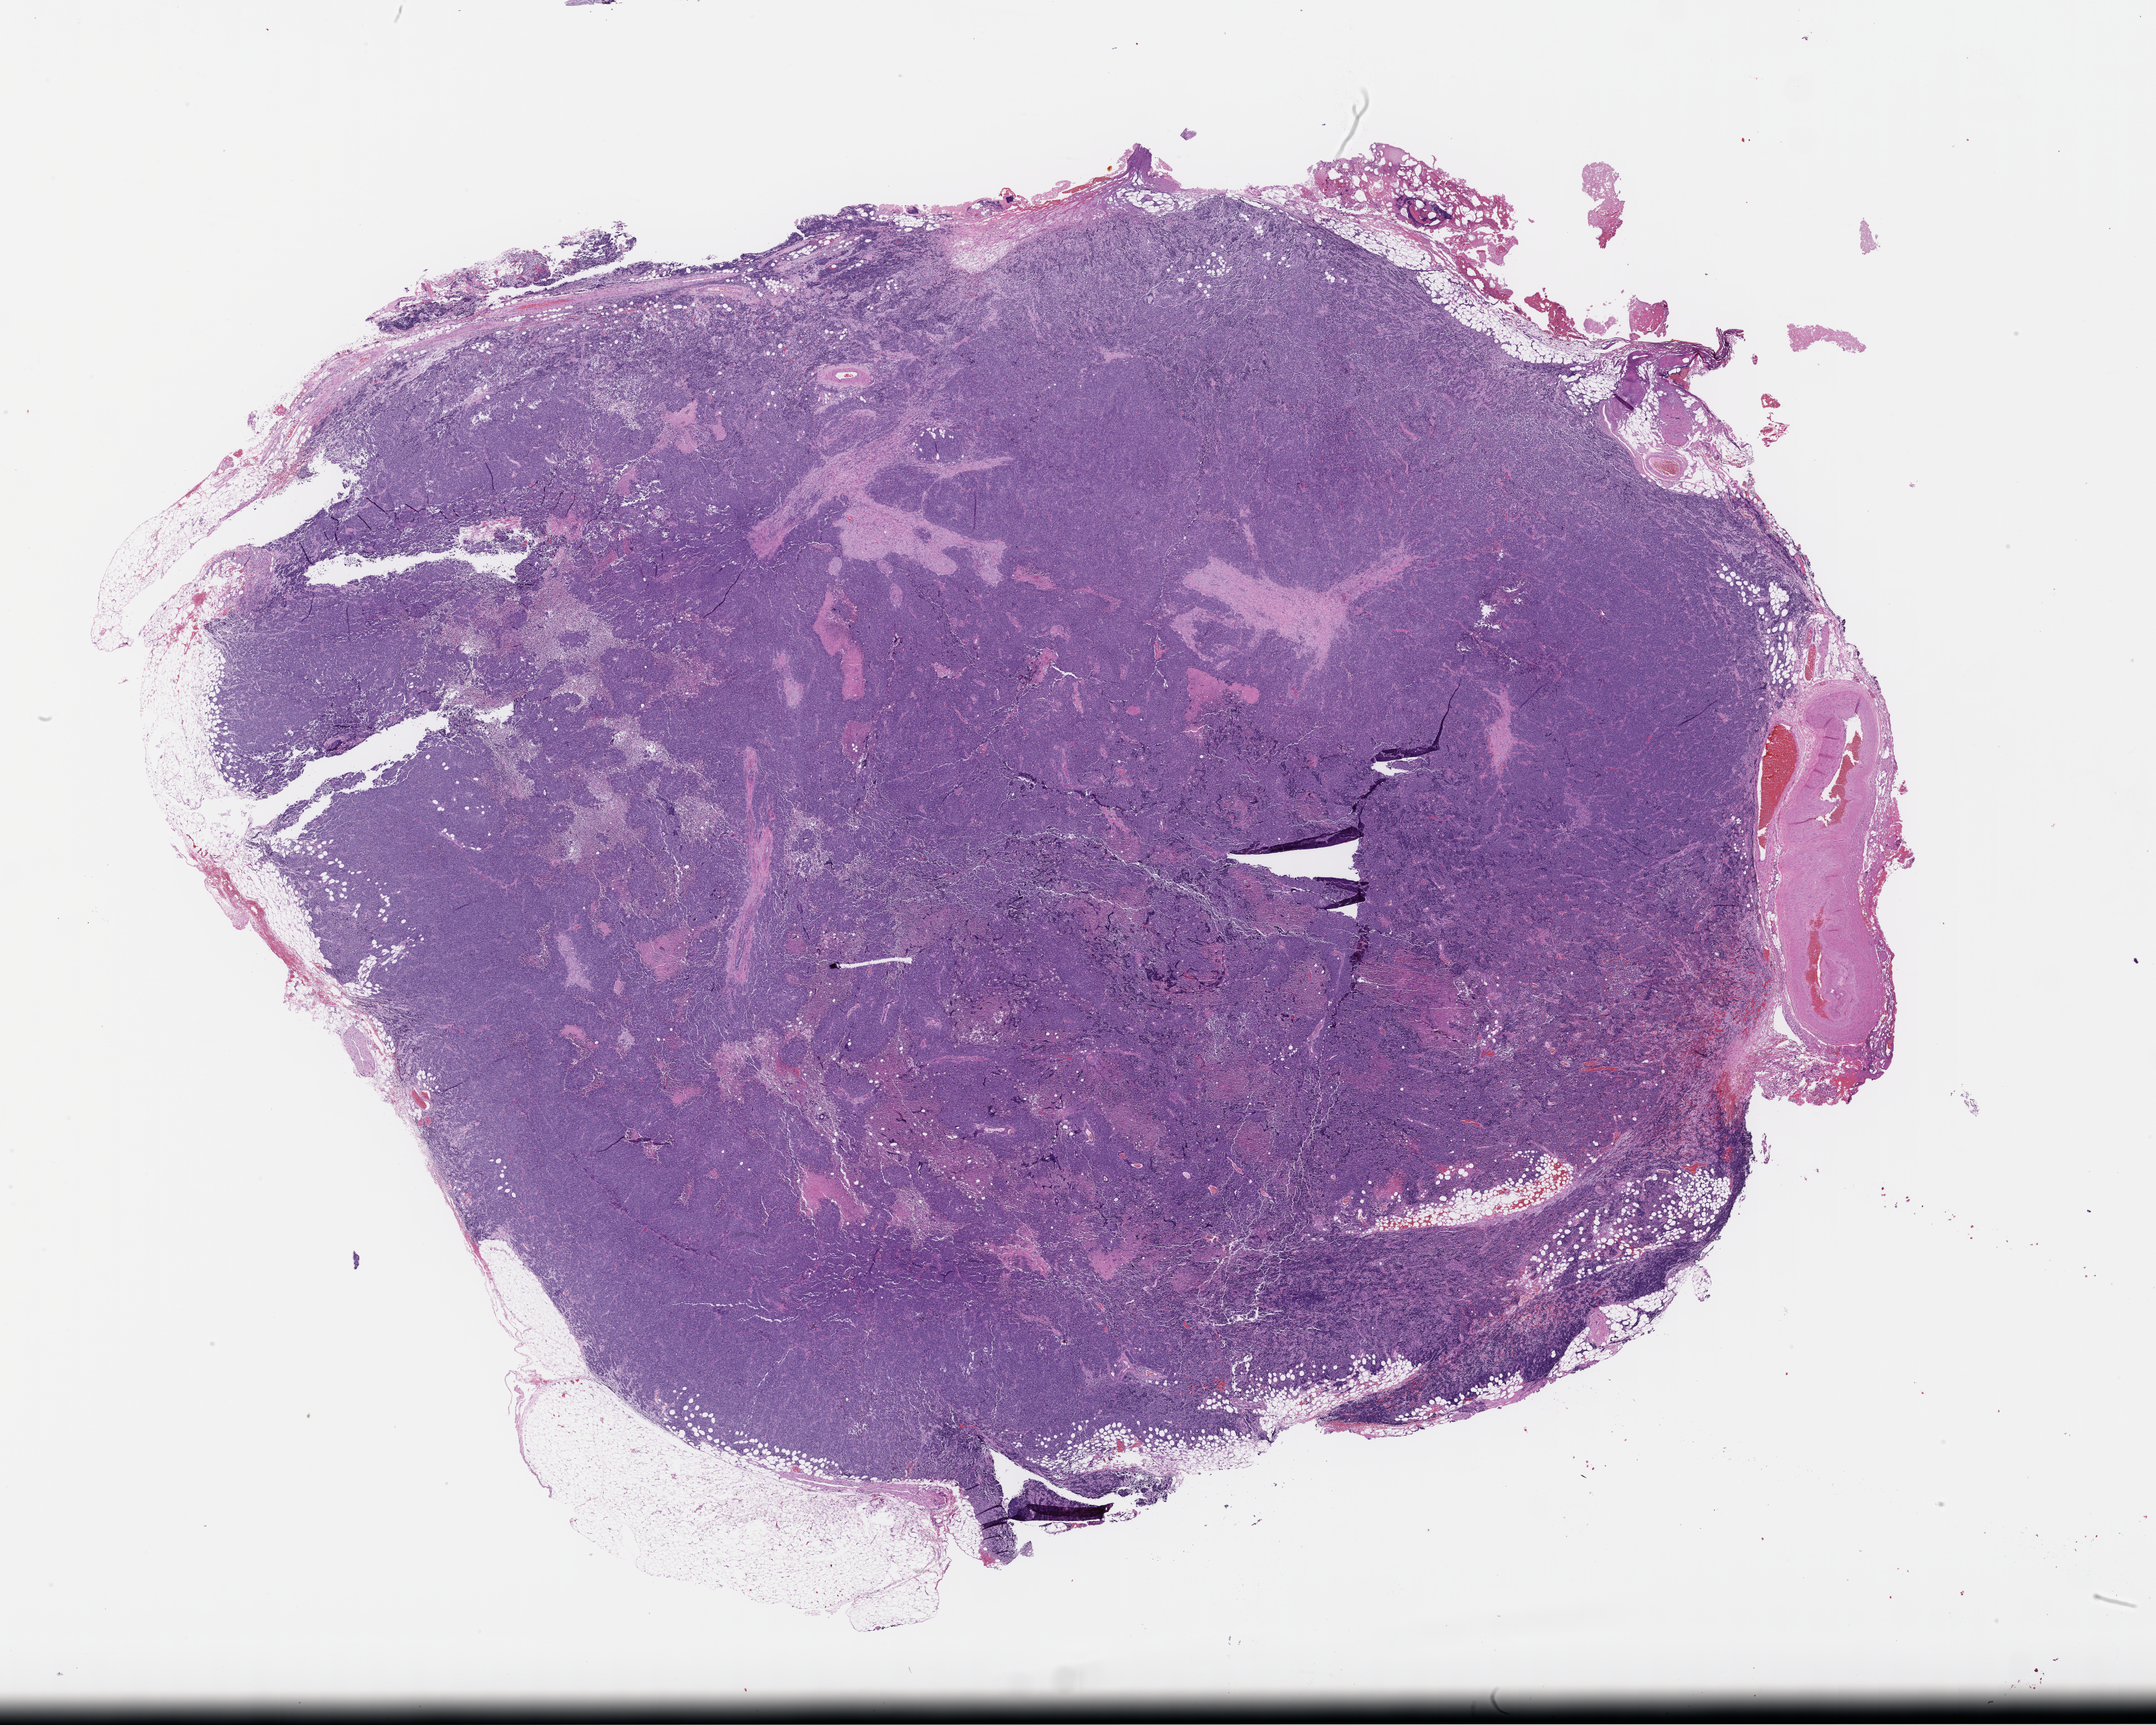
Haematoxylin and eosin whole-slide image — a low-resolution overview of the entire scanned area, about 27.1 x 21.7 mm; FFPE section. Female patient.
This section: metastasis (sampled organ not recorded). Patient diagnosis (primary): Small Cell Lung Carcinoma.